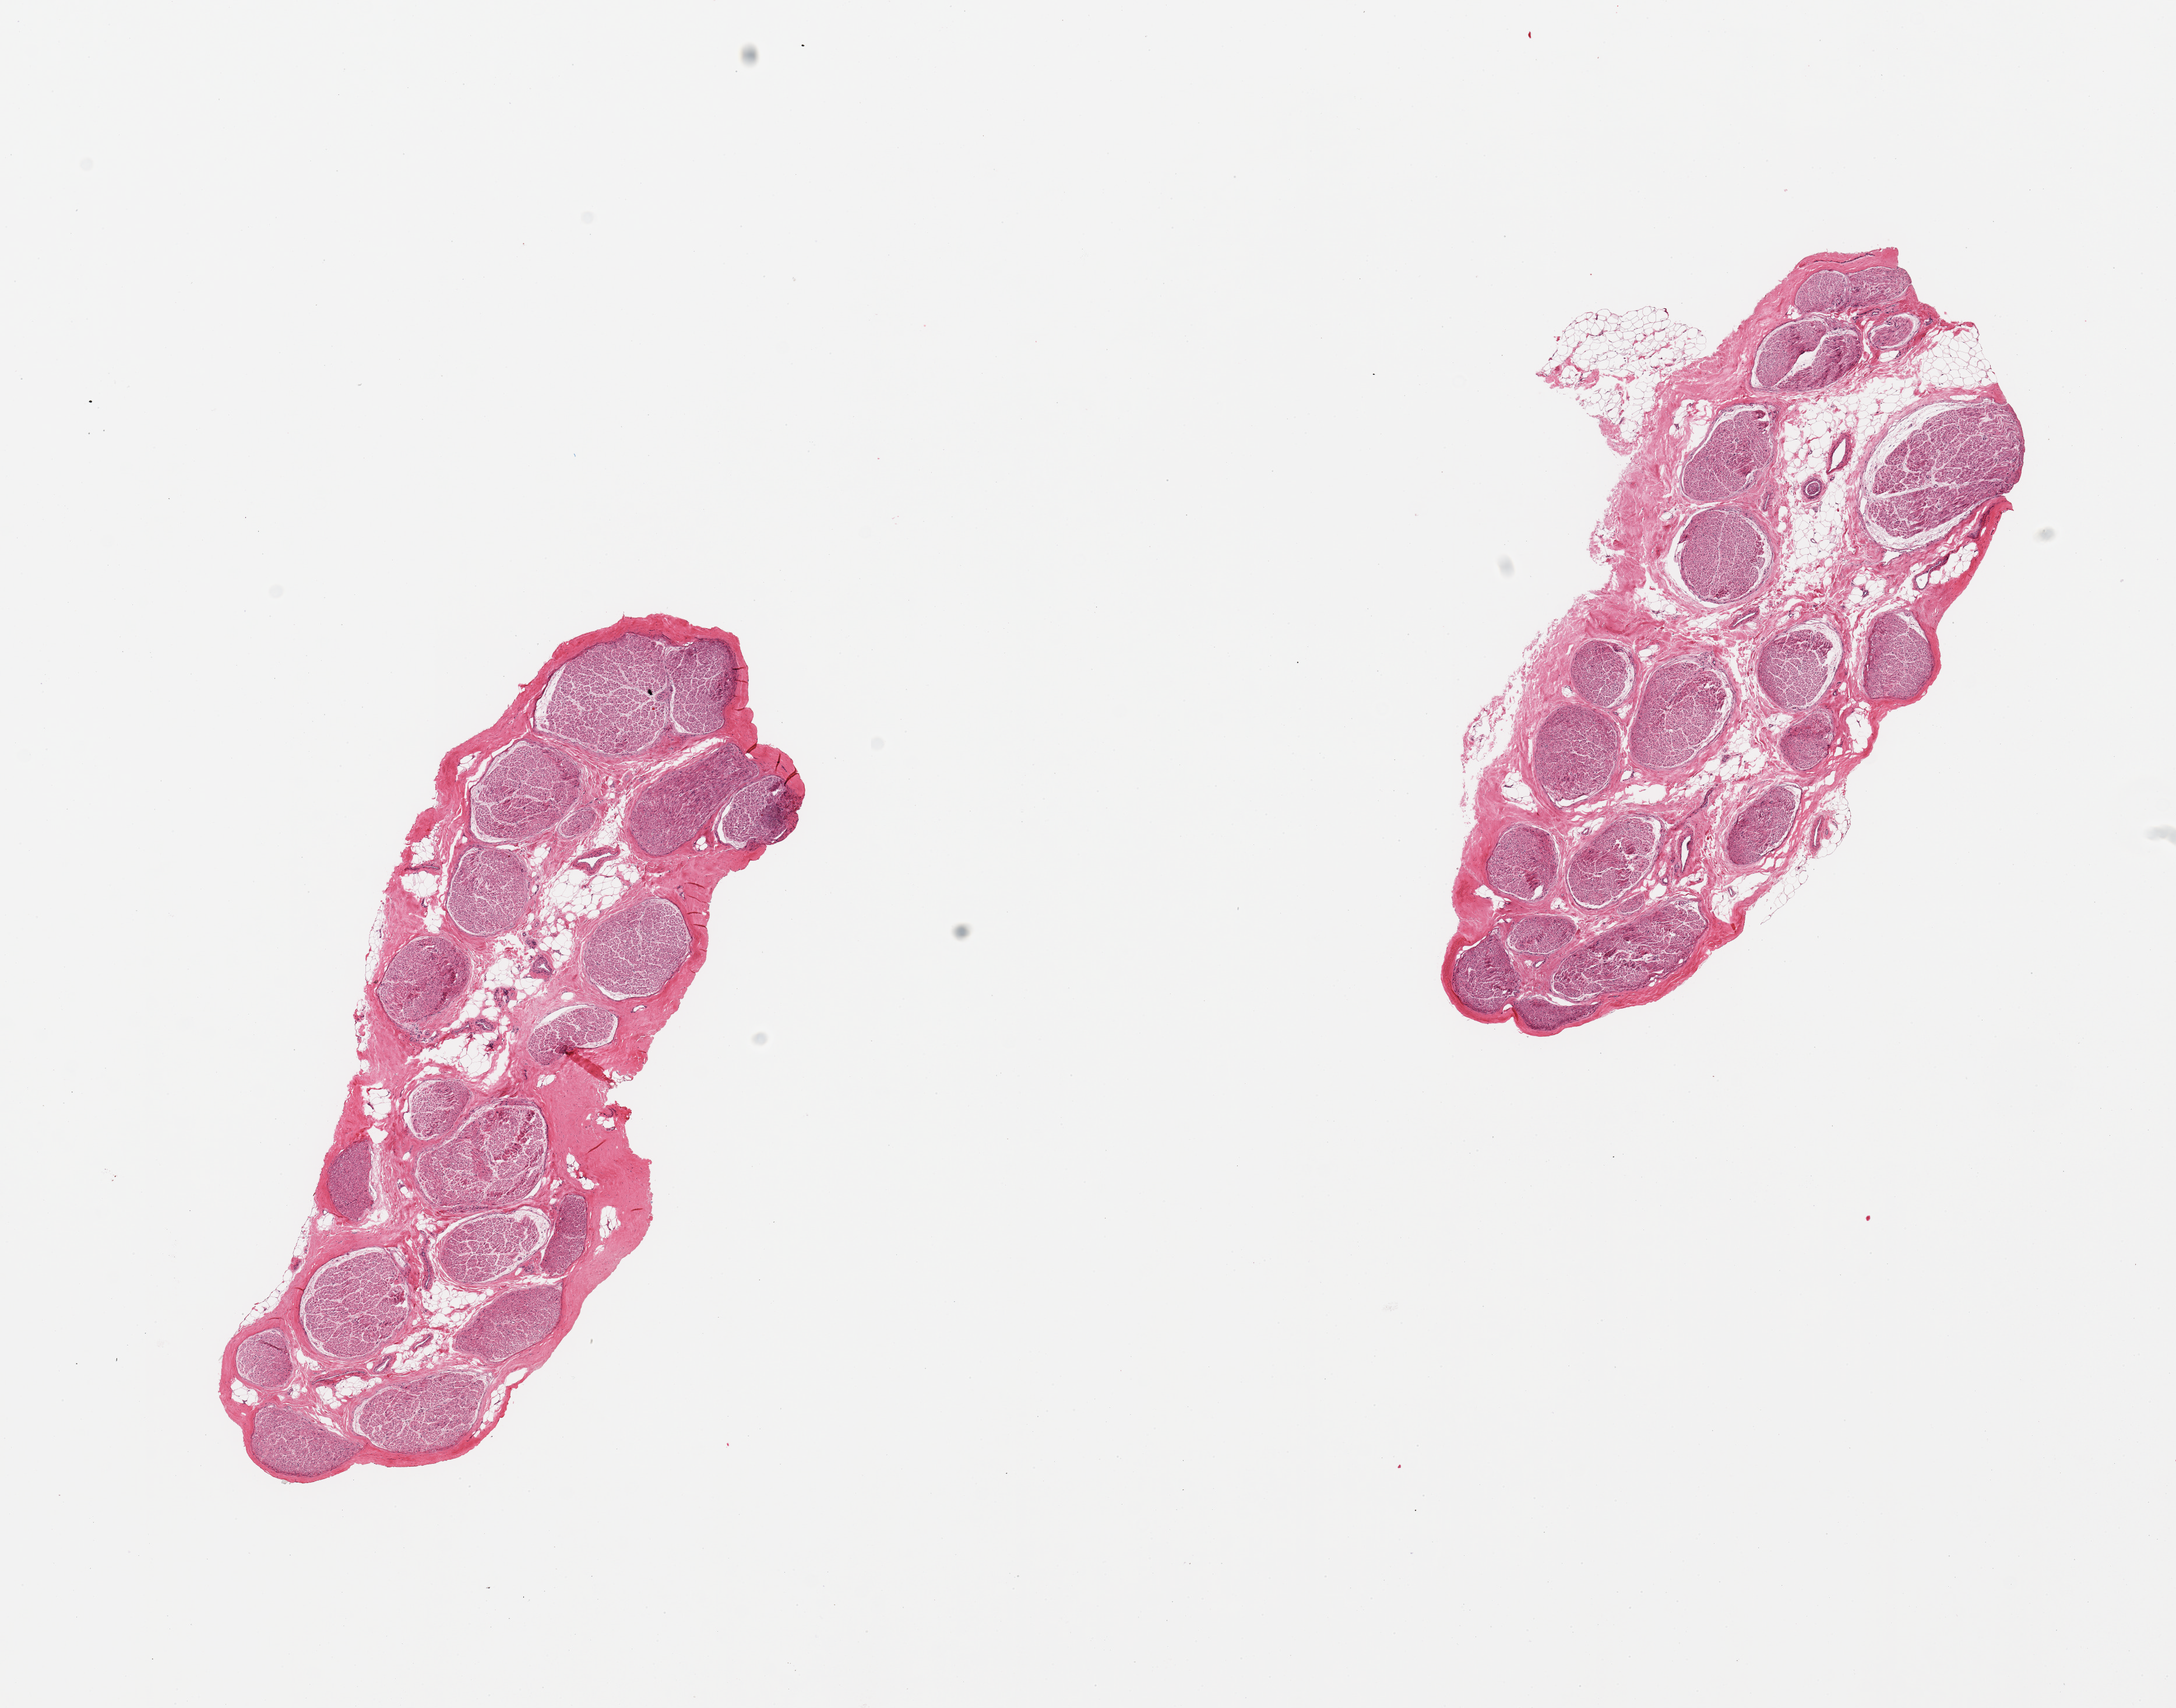
Haematoxylin and eosin whole-slide image — whole scanned area (about 14.8 x 11.6 mm, slide scanned at 20x) shown as a low-resolution overview; PAXgene-fixed paraffin-embedded (PFPE) section; target tissue: tibial nerve; donor tissue sample.
Reviewer comment on this tissue sample: 2 pieces; 10% internal fat content.